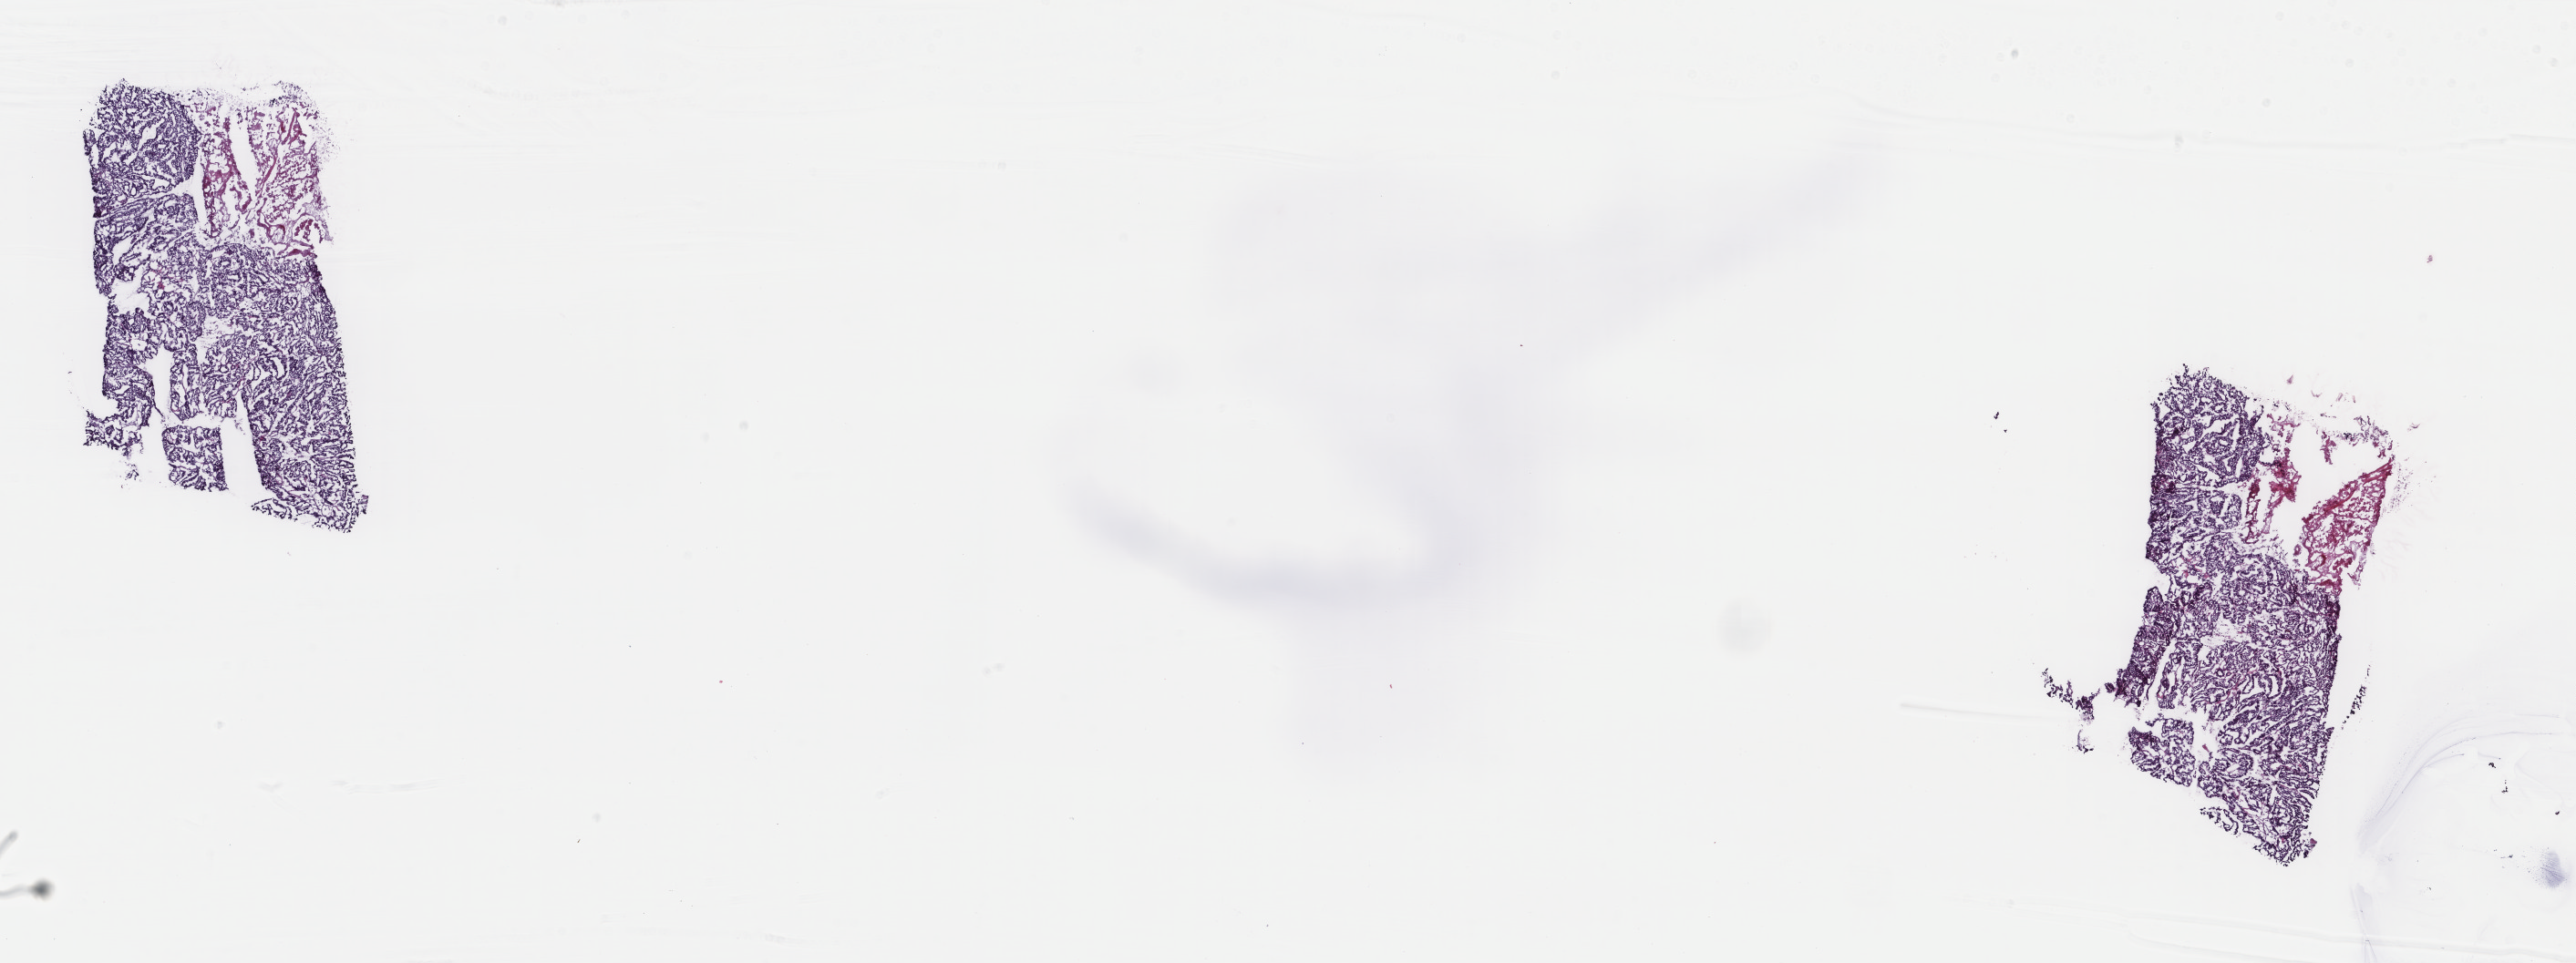
Whole-slide histology image, H&E — shown as a low-resolution overview of the whole scanned area (about 22.4 x 8.4 mm, acquisition: 40x scan). Frozen section from the top of the tissue portion. Uterus, primary tumour sample. Female patient; age at initial diagnosis 62 years. Histologic grade: G2 (moderately differentiated). Slide review estimates, as recorded: tumour cells 78%, tumour nuclei 98%, normal cells 0%, stromal cells 2%, necrosis 20%. Infiltration values recorded for this section: lymphocyte infiltration 2%, monocyte infiltration 1%, neutrophil infiltration 2%.
• FIGO stage: IA
• pathologic diagnosis: Endometrioid adenocarcinoma, NOS (endometrium)